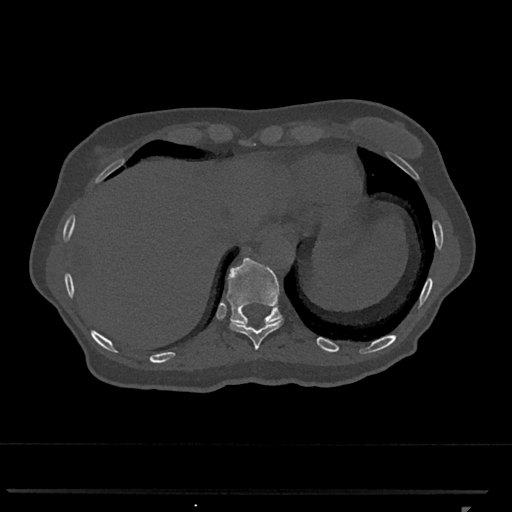
CT including the spine, one axial slice. Position 548 of 793 along the scan axis. Bone window (W 1800 / L 400 HU). 0.5 mm slice thickness. 512 × 512 image matrix, field of view 380 × 380 mm. Patient: female, 62 years. From the clinical record (not read from this slice): primary cancer: renal.
Outlined on this slice (semi-automatically segmented with operator editing):
- T10 vertebra: box from (x=230, y=319) to (x=283, y=350) px
- T11 vertebra: (x=226, y=258)–(x=283, y=326)